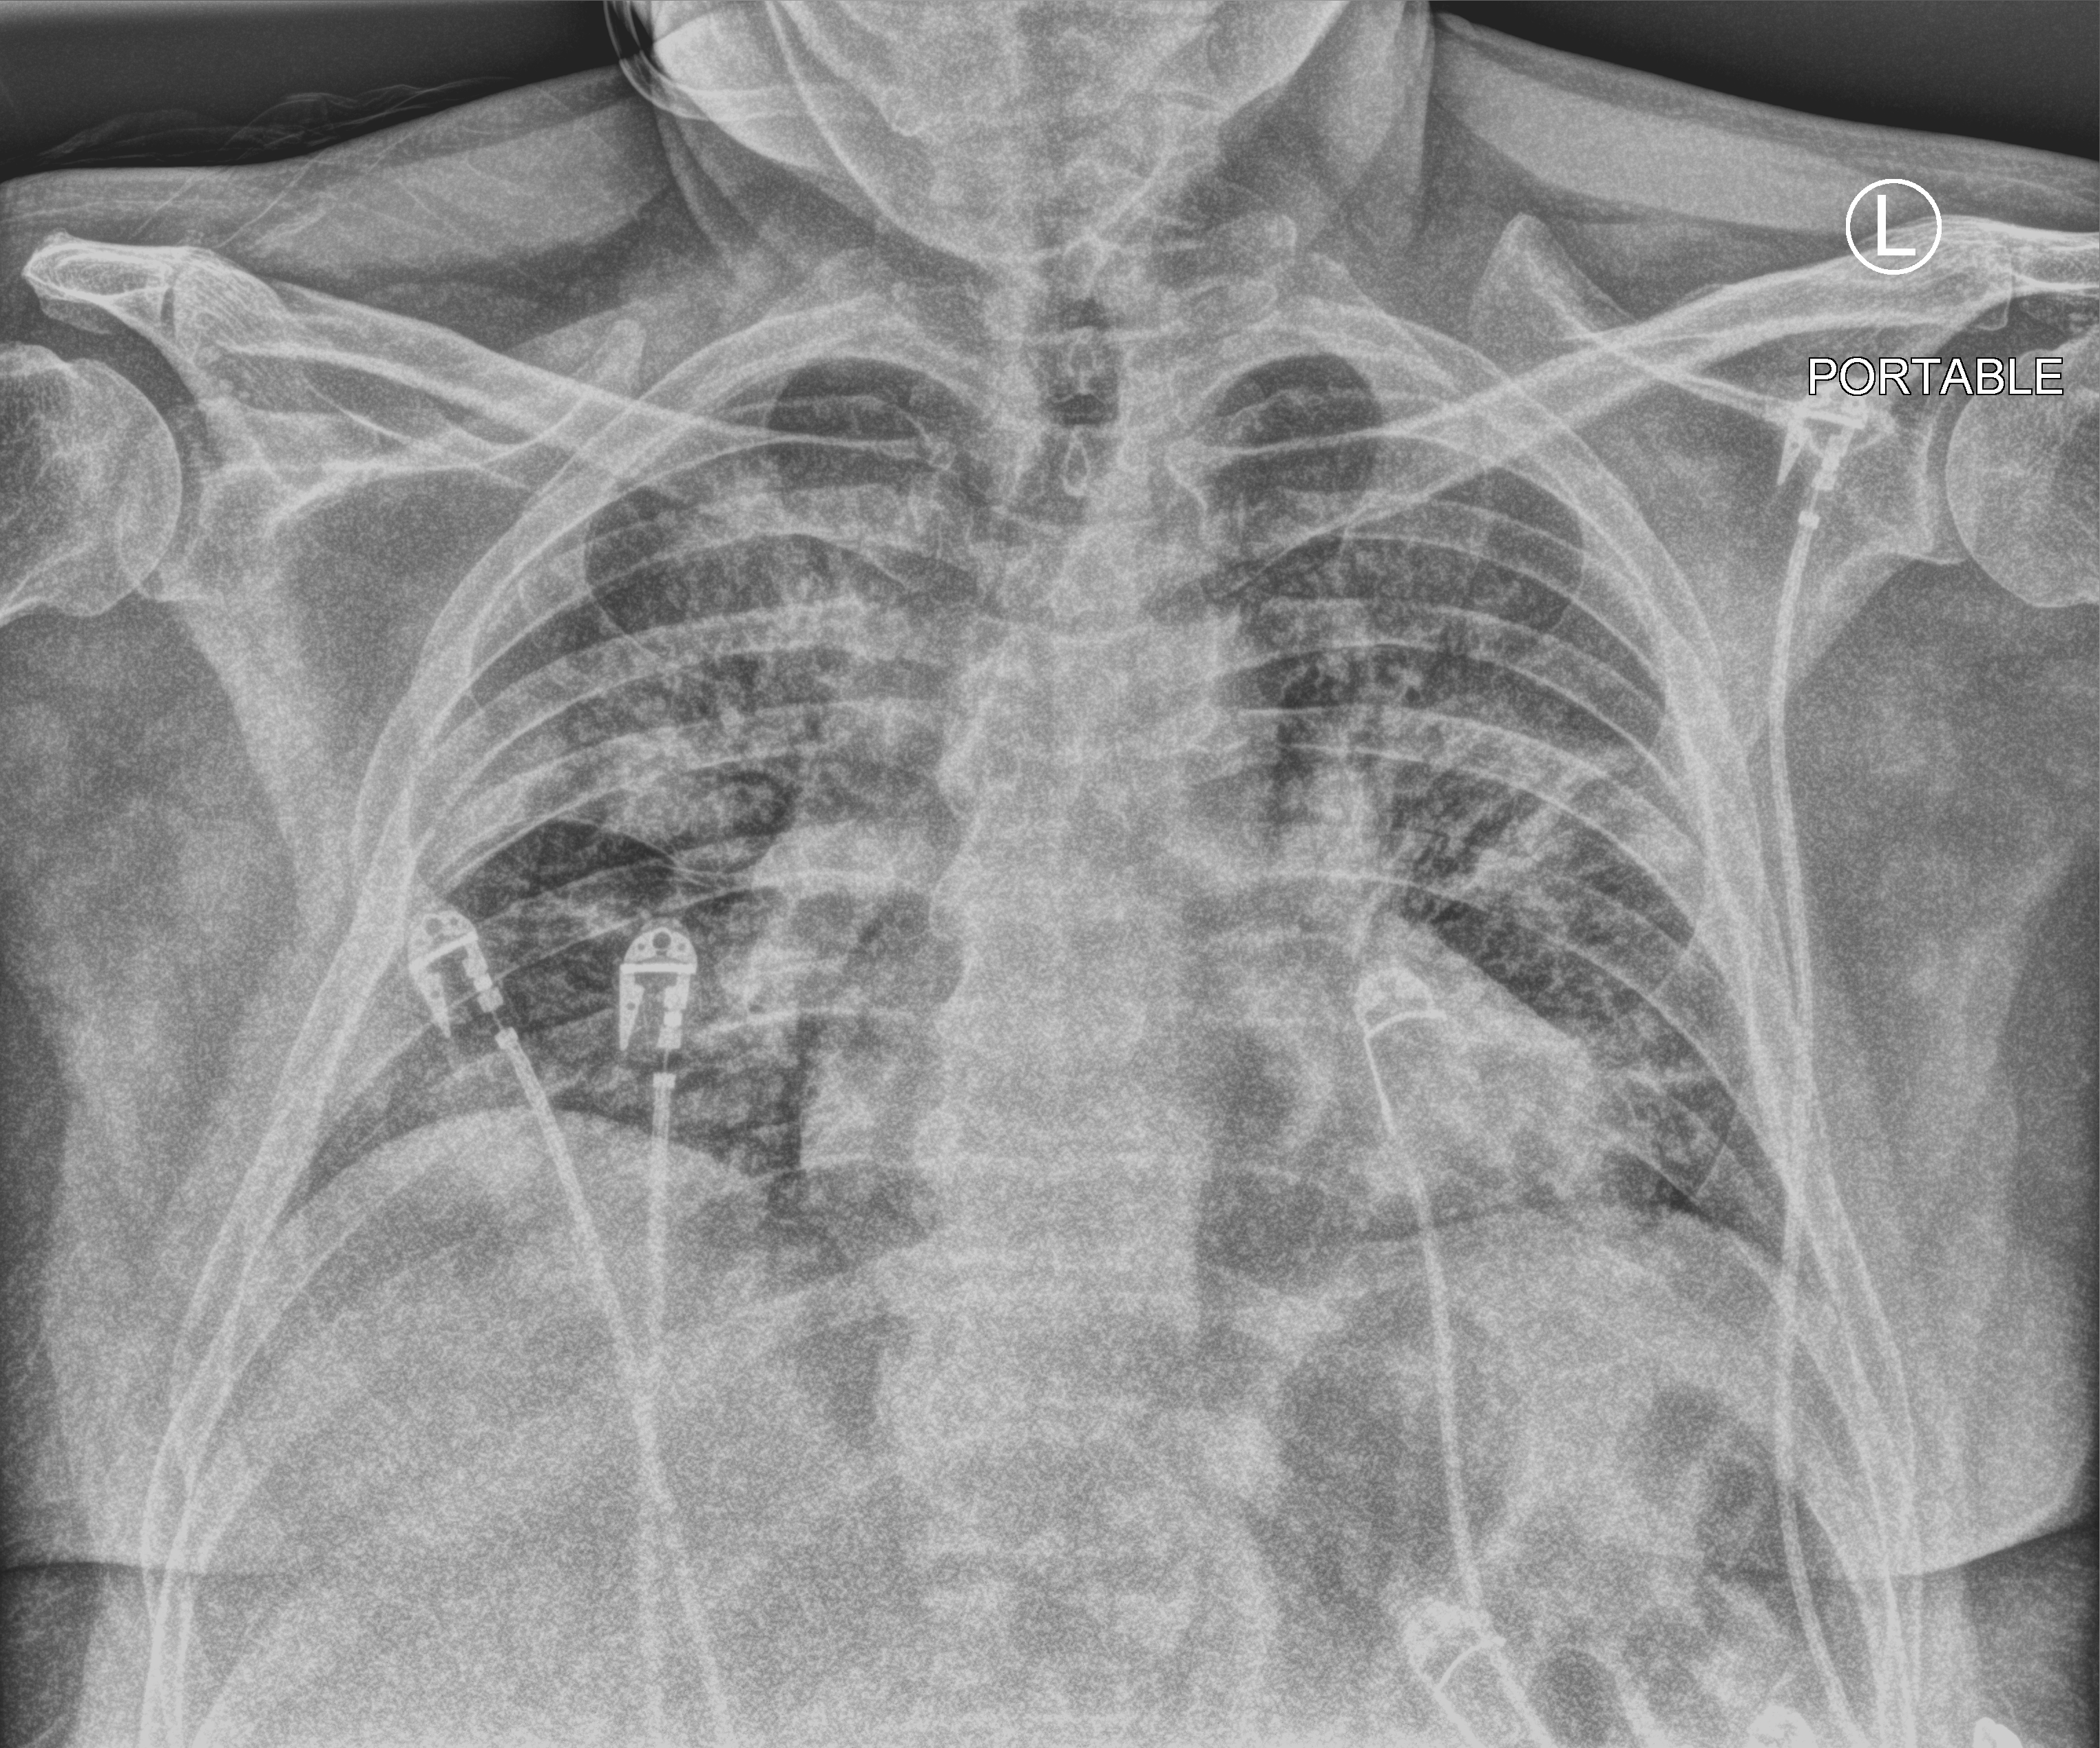
Portable chest radiograph, anteroposterior (AP) projection. Patient hospitalised with COVID-19; male, aged 60–74 years.
Admission-level facts for this patient (not findings on this image; timing relative to this image not recorded):
- mechanically ventilated during this hospital stay: yes
- chronic kidney disease (admission record): no
- admitted to intensive care during this hospital stay: yes